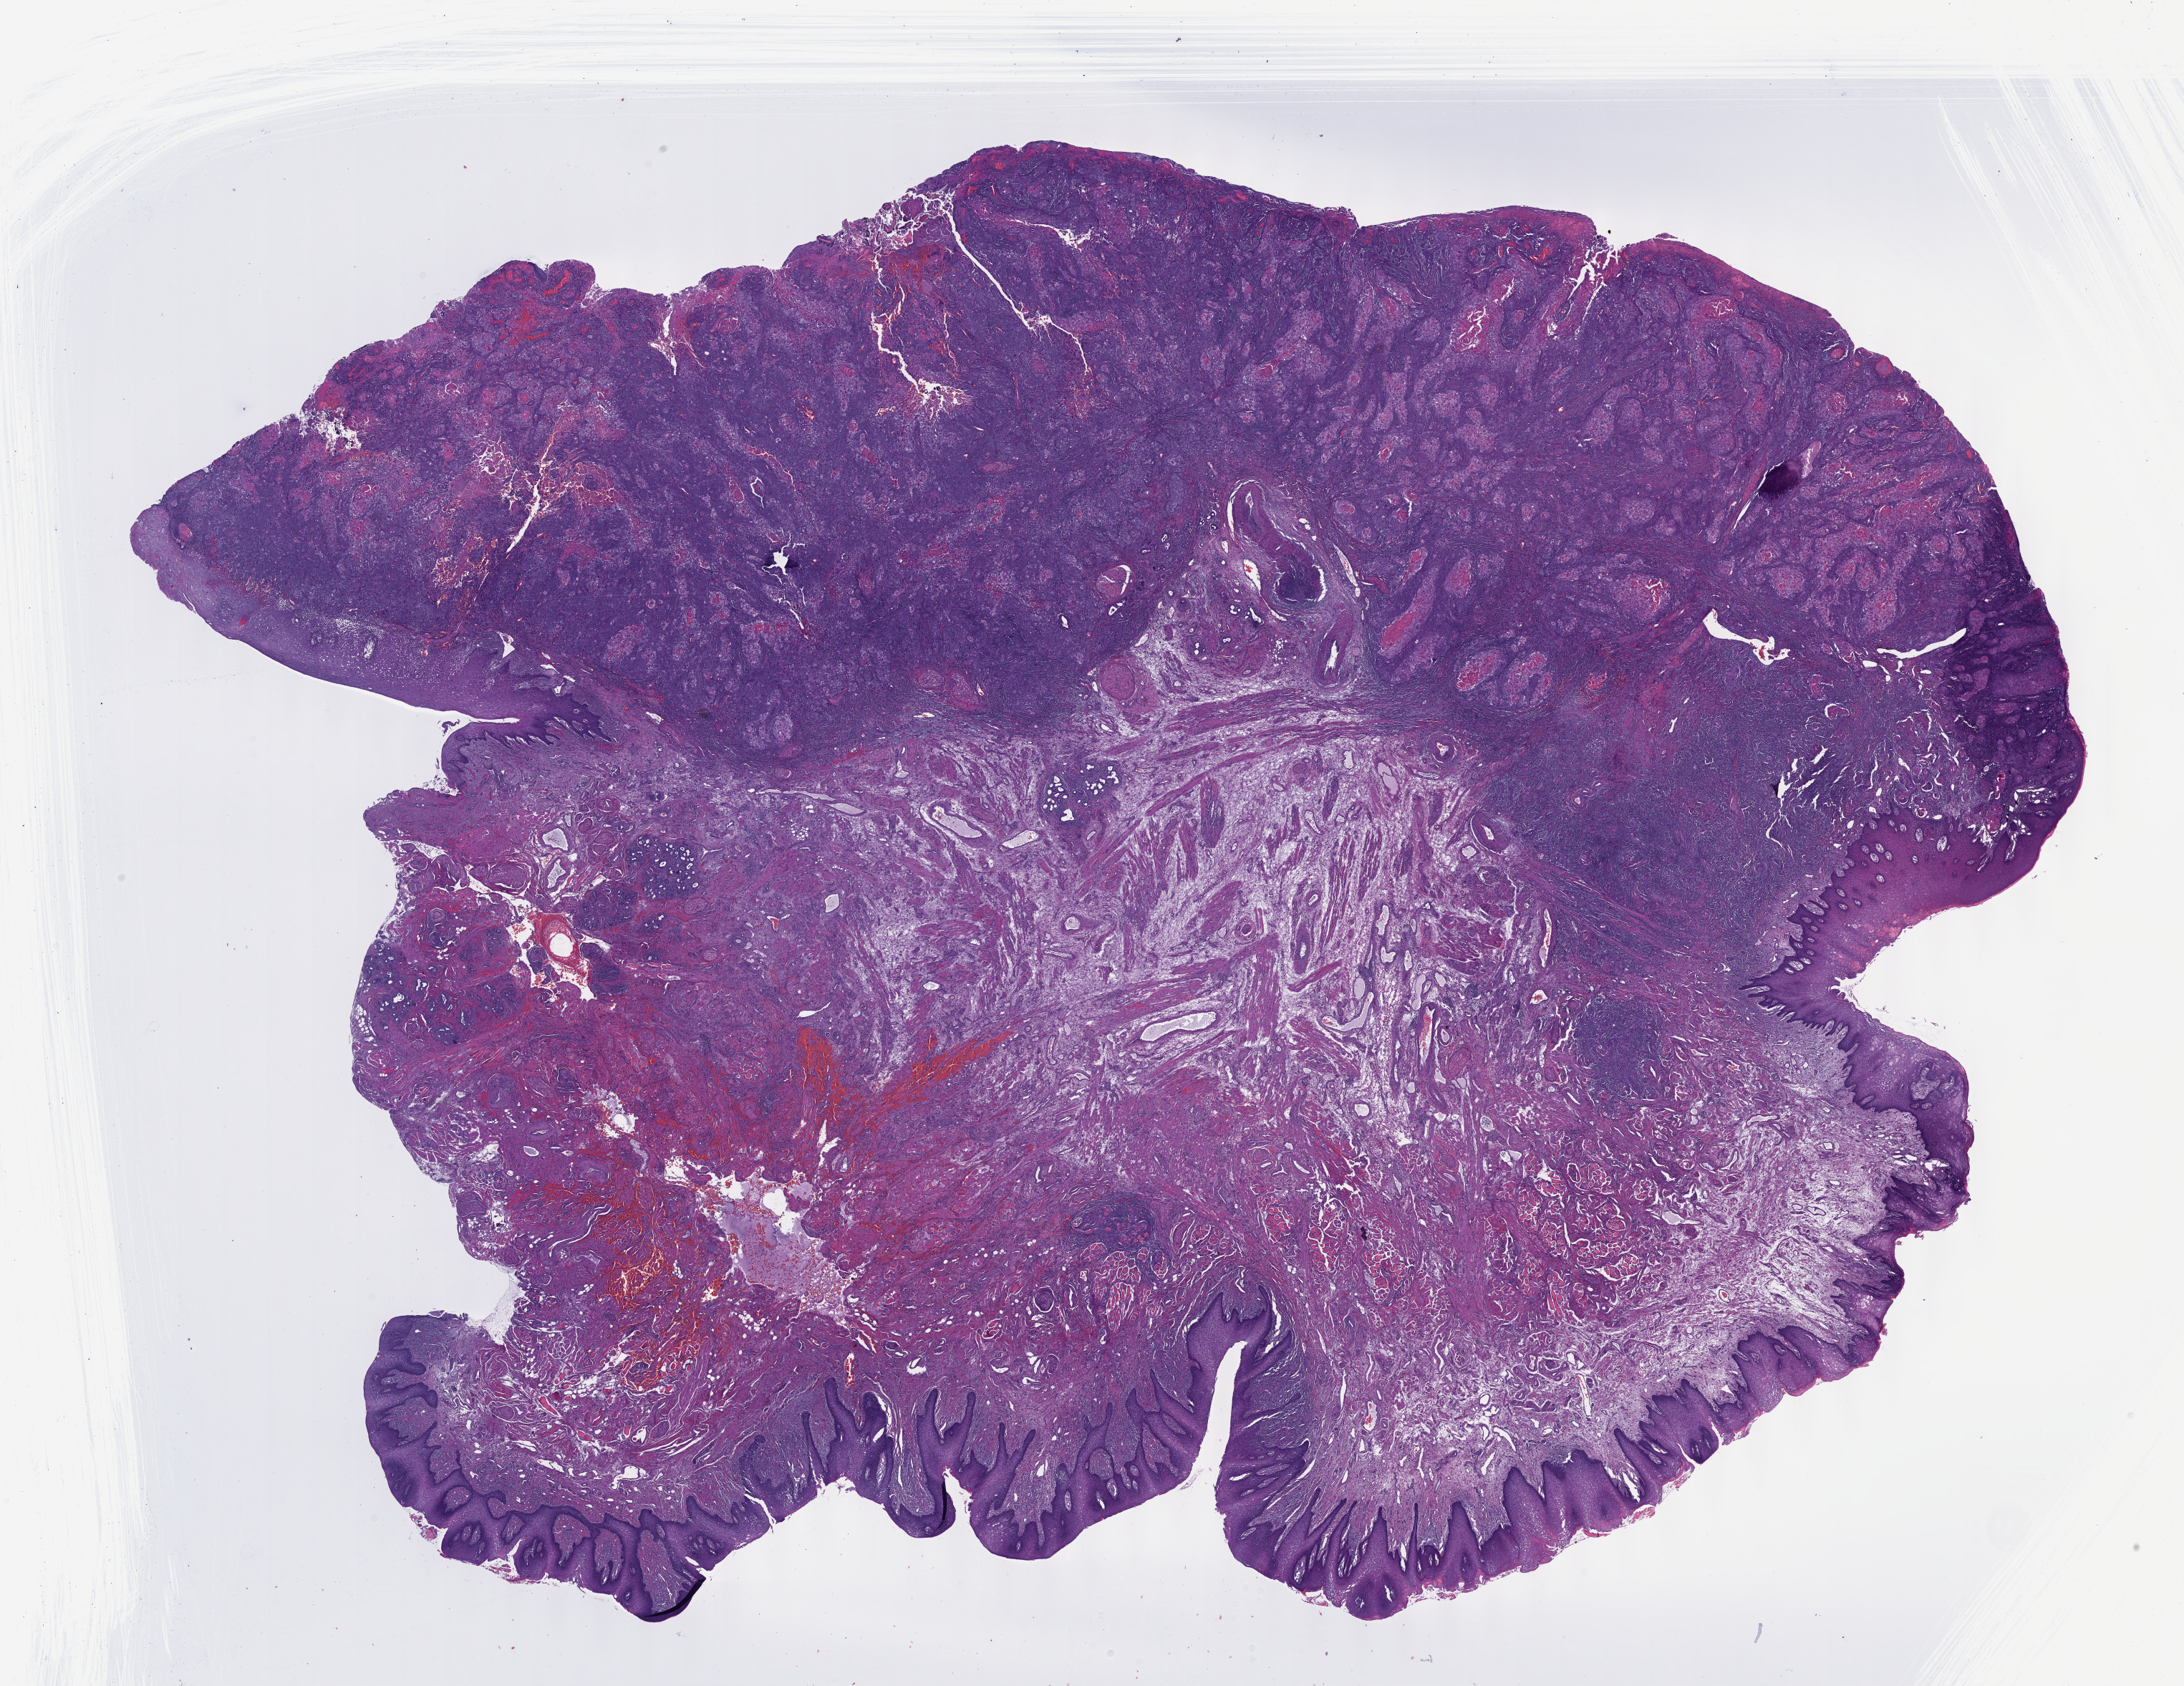
H&E-stained whole-slide image, whole scanned area (about 24.6 x 19.0 mm, from a 40x scan) shown as a low-resolution overview. Formalin-fixed paraffin-embedded (FFPE) diagnostic section. Head and neck, primary tumour sample. Male, age 66 years at initial diagnosis. Histologic grade: G2 (moderately differentiated).
* TNM: T3 N2b
* AJCC pathologic stage: IVA (7th edition)
* pathologic diagnosis: Squamous cell carcinoma, NOS